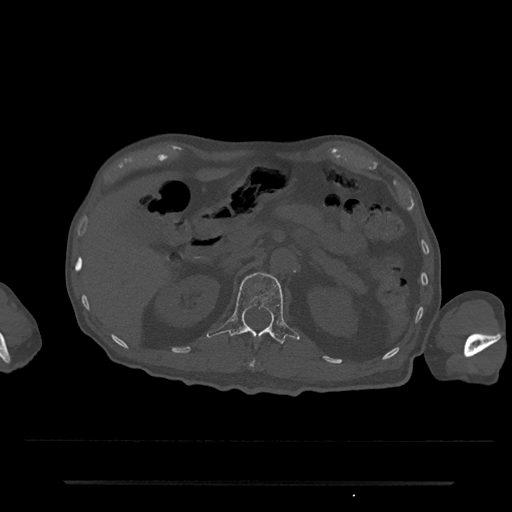
CT including the spine, one axial slice; position 140 of 797 along the scan axis; 120 kVp; bone window (W 1800 / L 400 HU); 0.5 mm slice thickness; 512 × 512 image matrix, field of view 427 × 427 mm. Patient: male, 74 years. From the clinical record (not read from this slice): primary cancer: prostate.
Annotated regions visible in this slice (semi-automatically segmented with operator editing):
- L1 vertebra: bounding box <207,272,300,344> (left, top, right, bottom; pixels)
- T12 vertebra: <248,361,255,368>